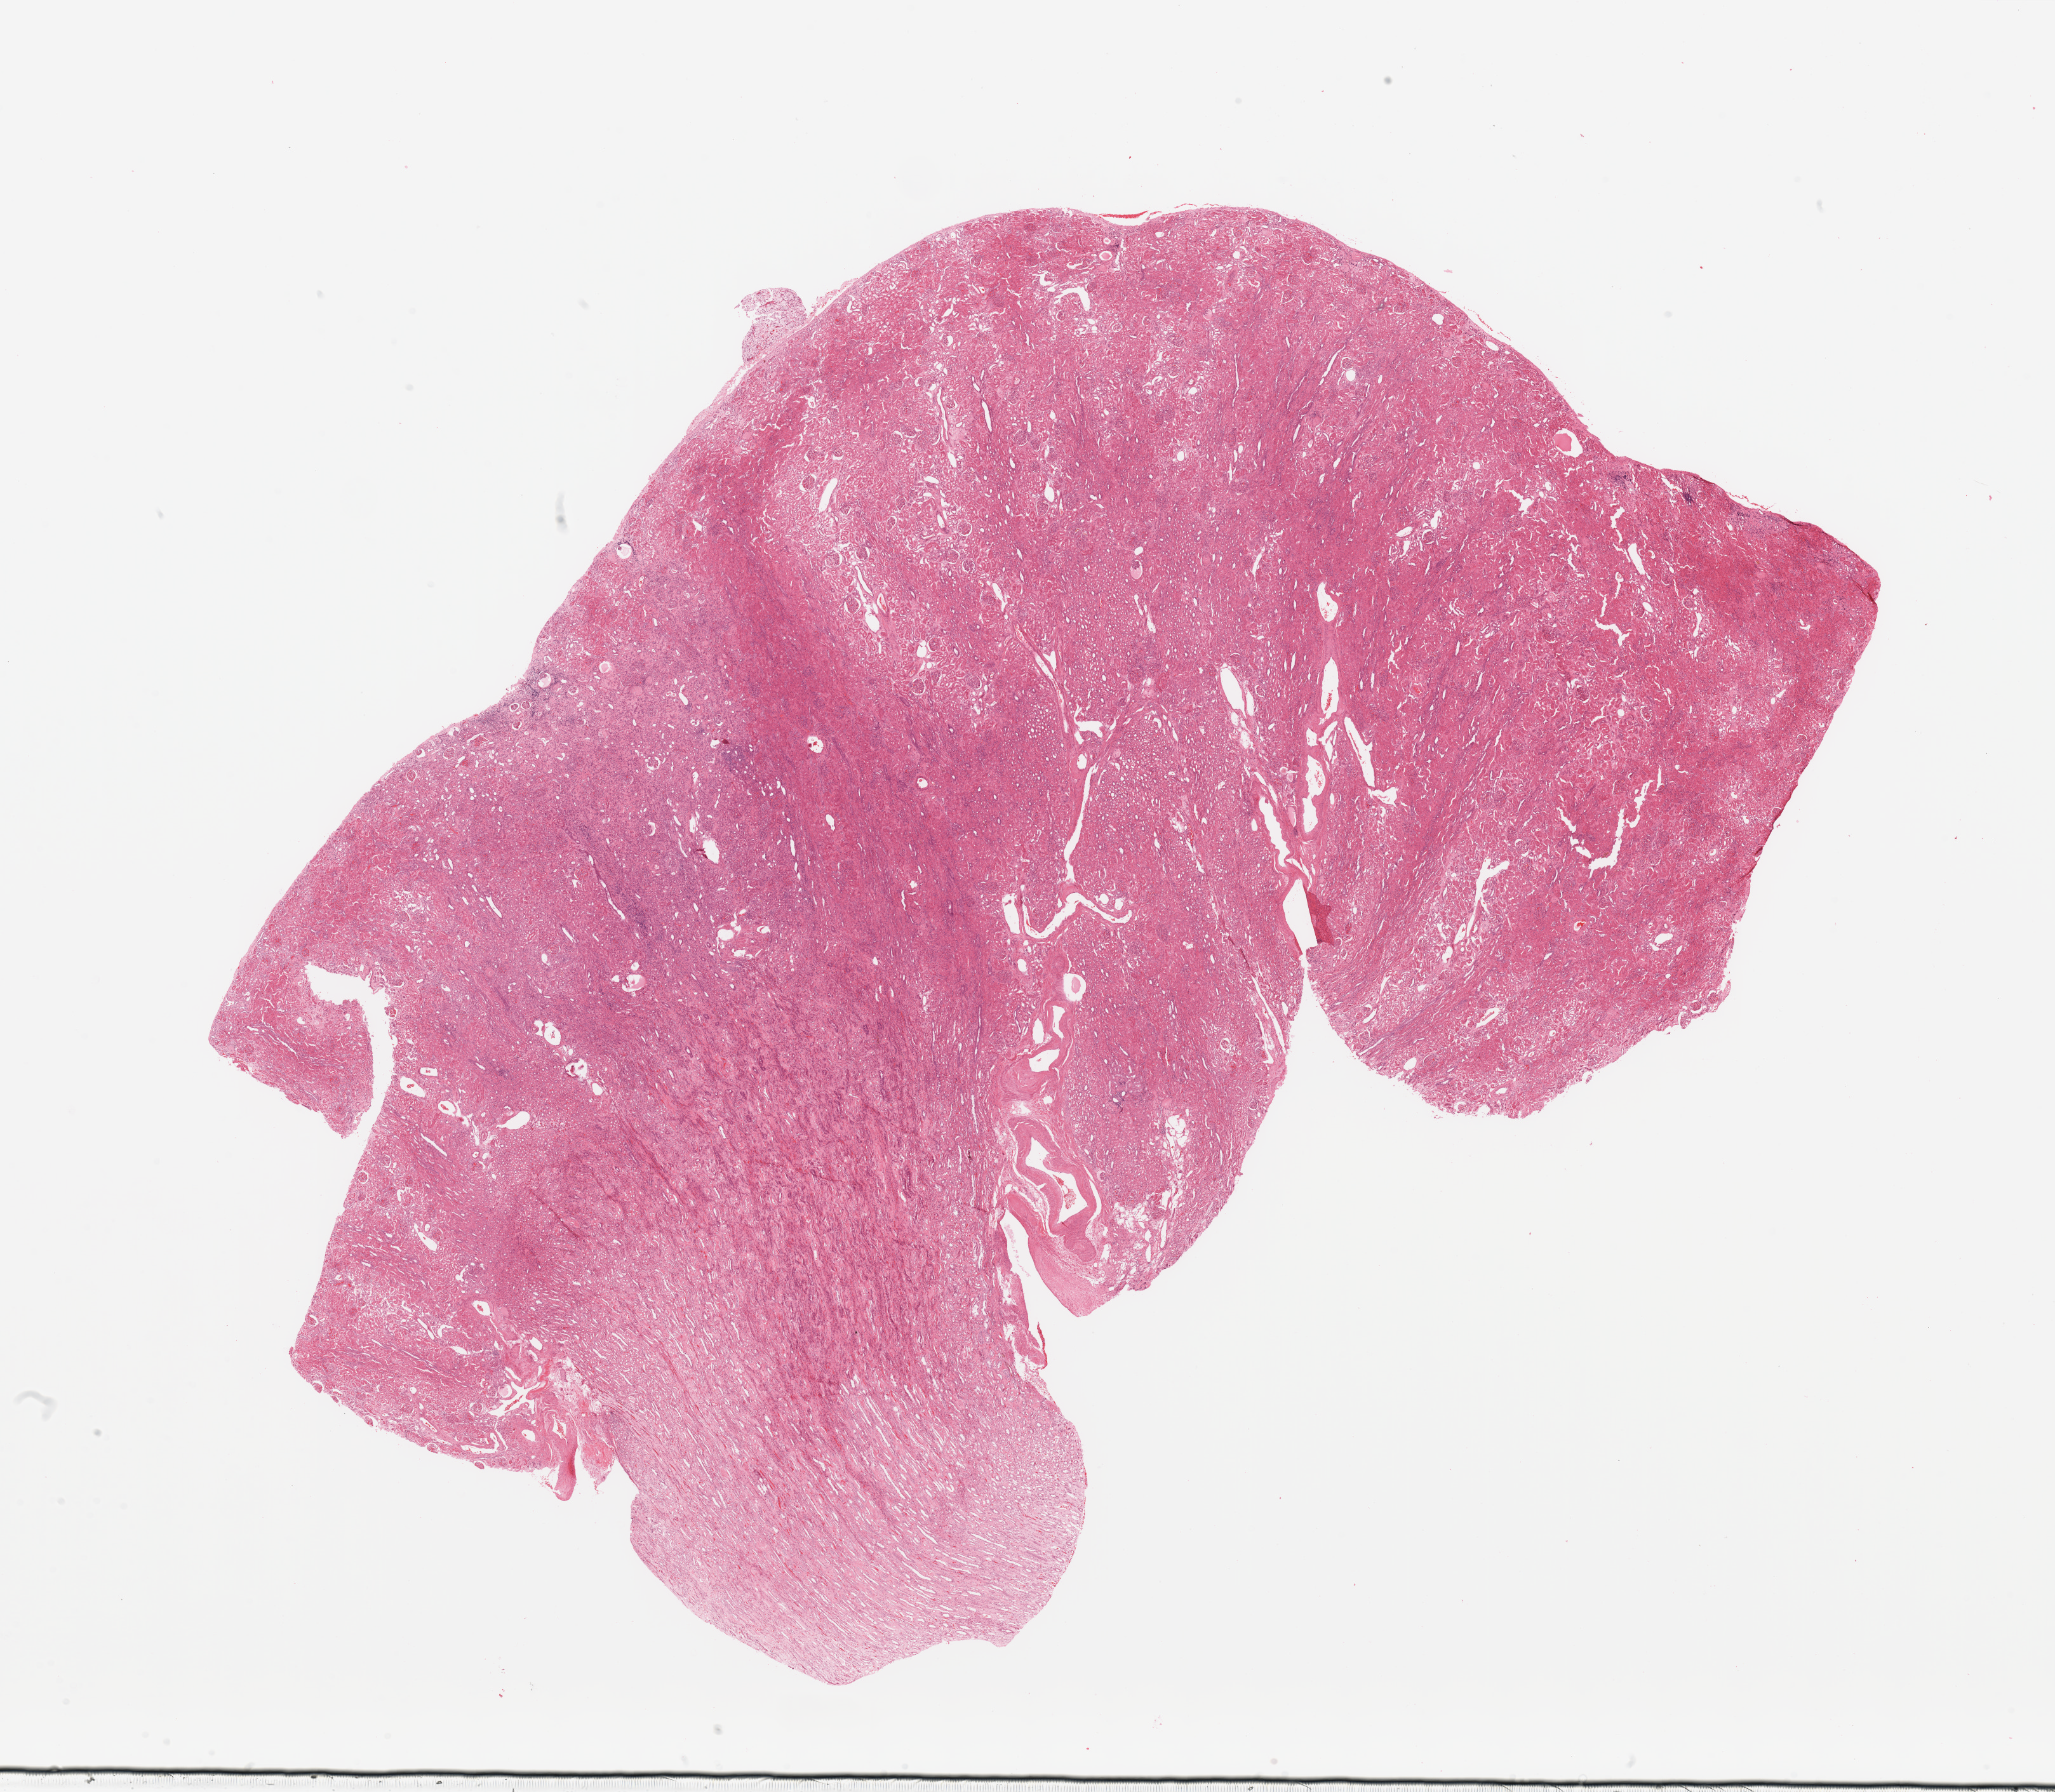
Digitized H&E-stained tissue section (whole slide), whole scanned area (about 25.6 x 22.3 mm) shown as a low-resolution overview, normal (non-tumour) tissue sample, sampled site: kidney. 66-year-old male patient.
This section: normal (non-tumour) tissue from the same patient. Patient diagnosis: Renal cell carcinoma, NOS.